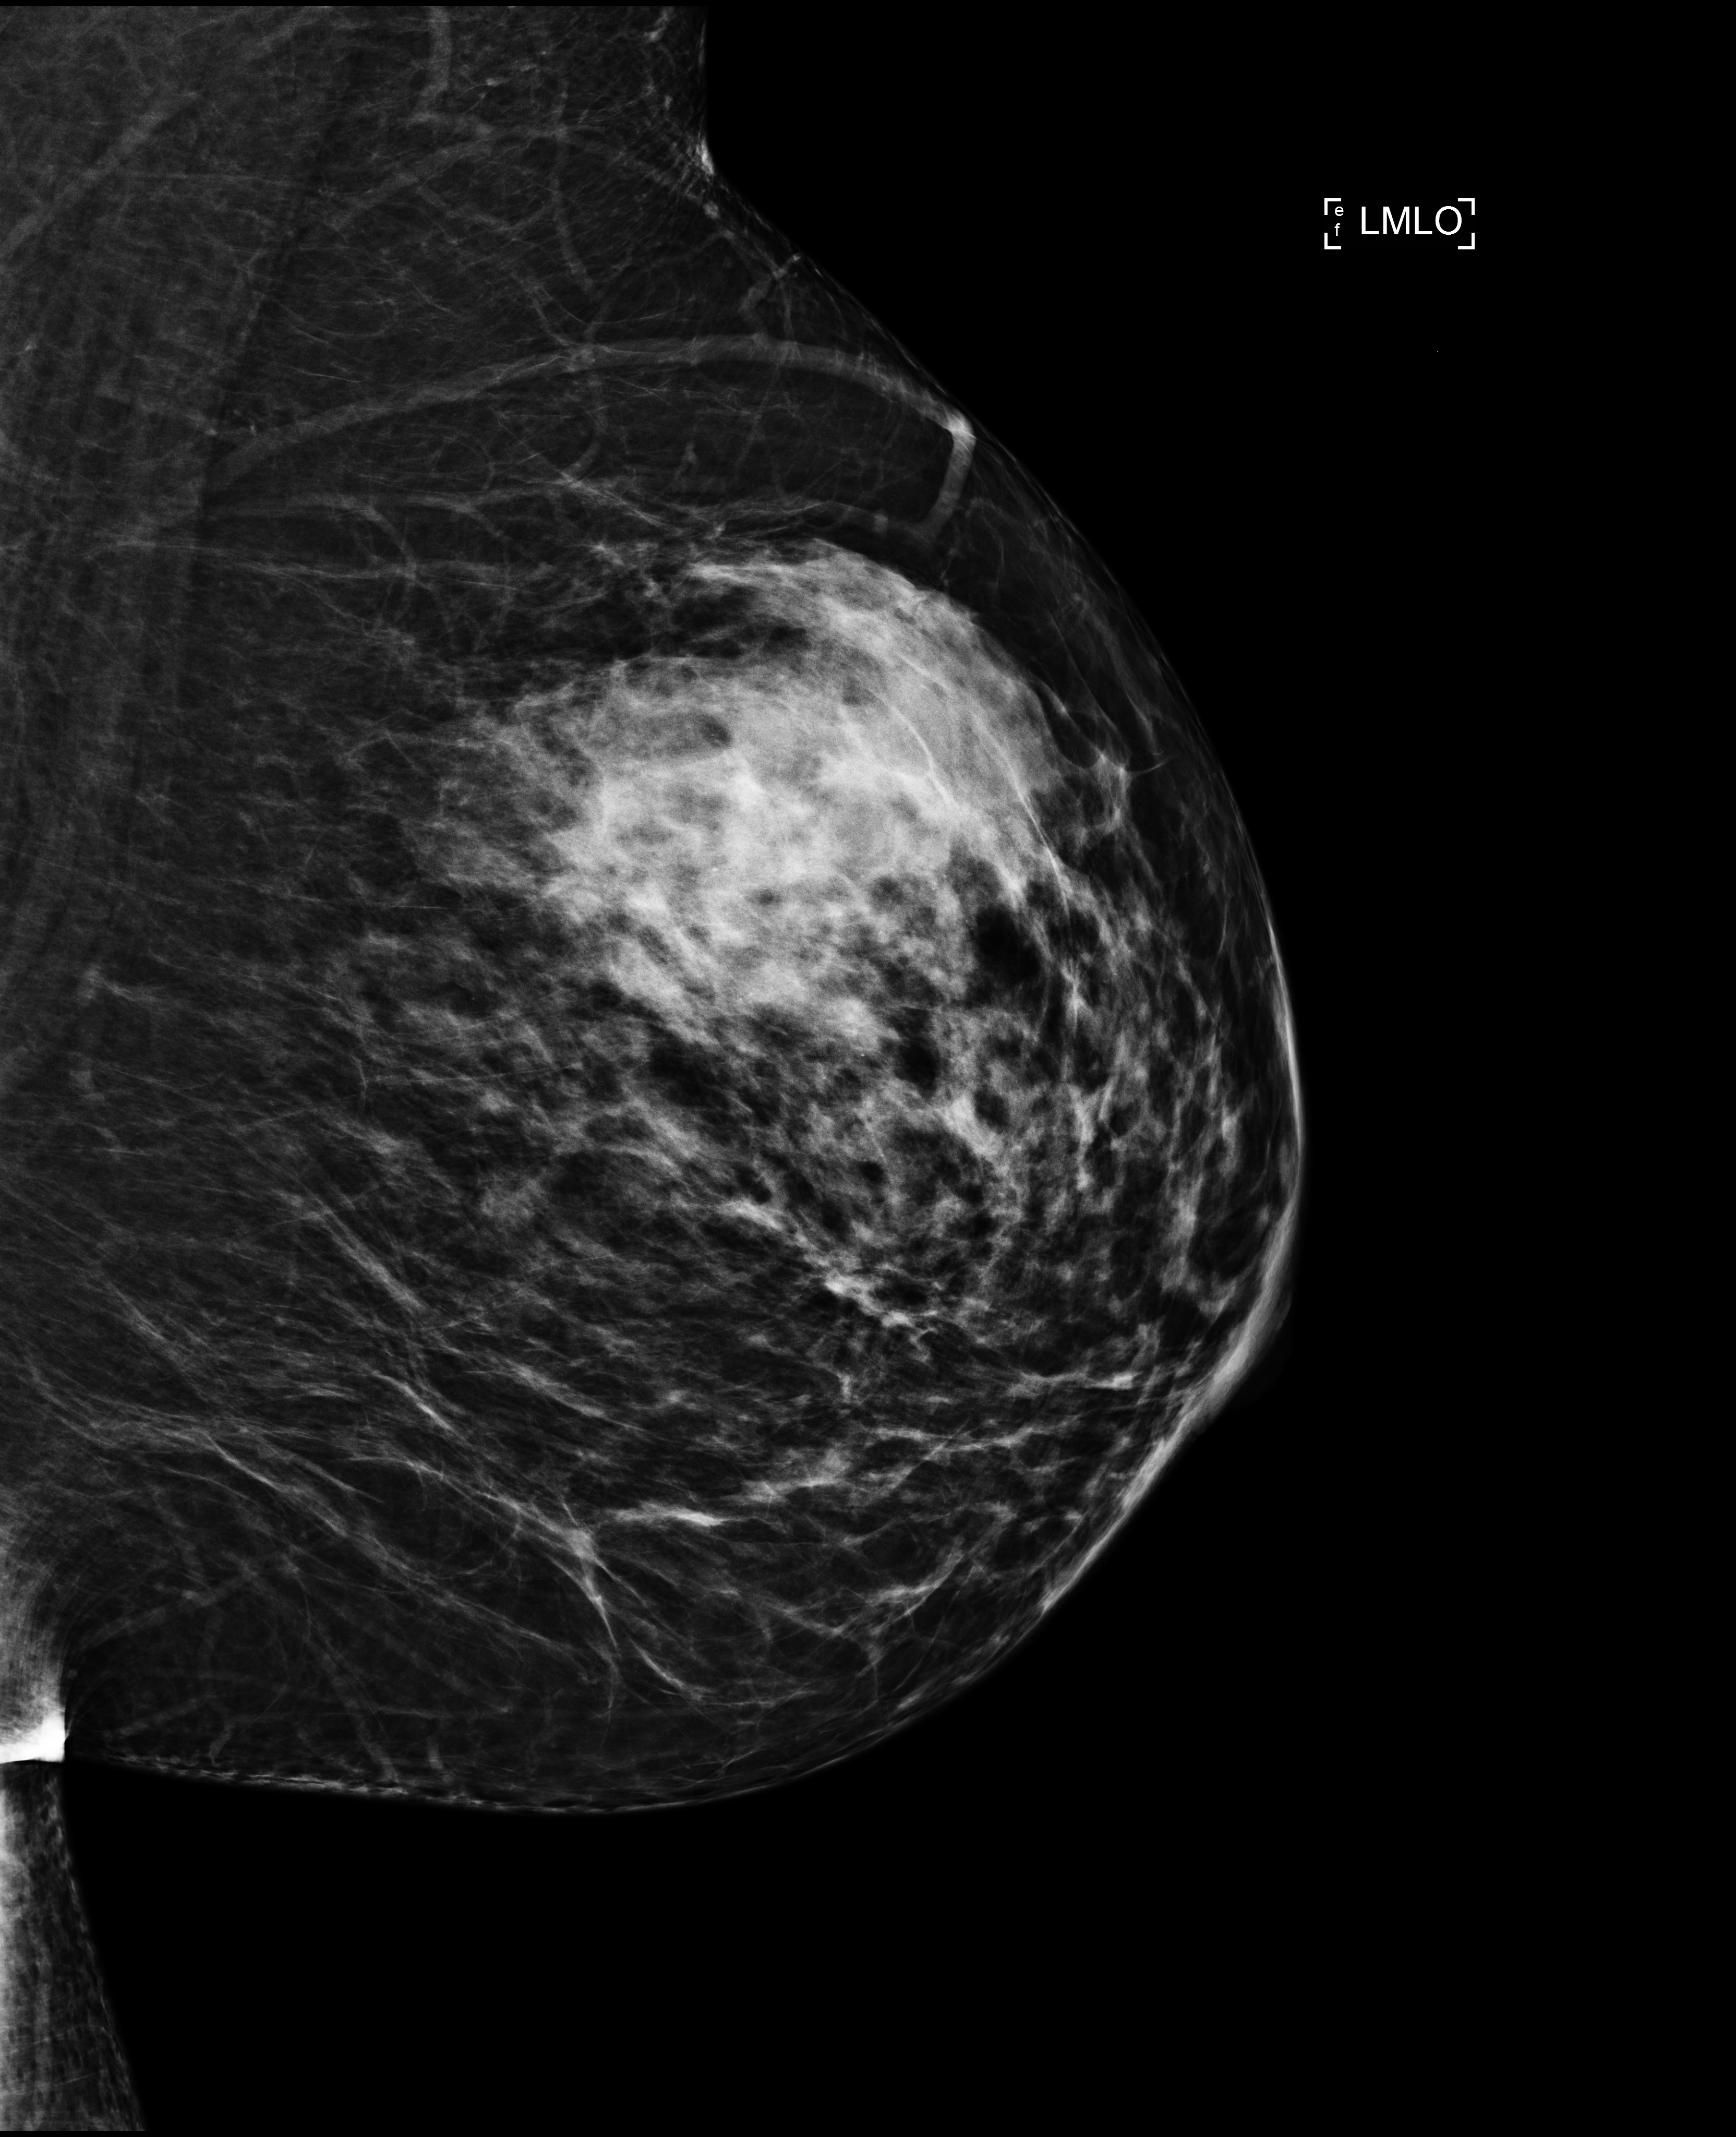
Digital mammogram (FFDM); left breast; mediolateral oblique (MLO) view; screening examination; system: Selenia Dimensions. Patient aged 49 years (female).
BI-RADS breast density category at the screening exam (both breasts, scale 1–4): 3. Final BI-RADS category for the screening round (tomosynthesis exam, both breasts): category 1. Recall: no recall after this screen.